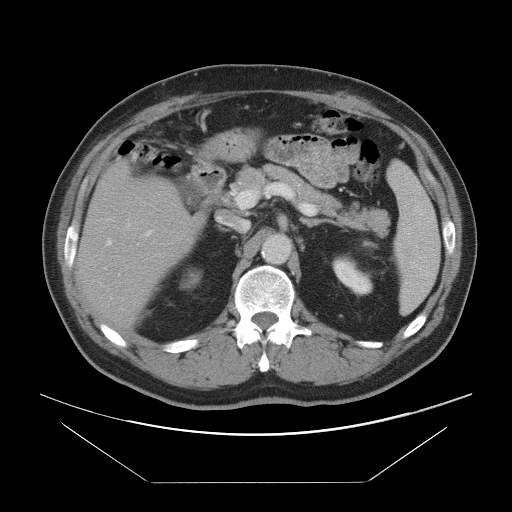
Contrast-enhanced abdominal CT, one axial slice. Position 50 of 97 along the scan axis. 120 kVp. Intravenous contrast given. Soft-tissue window (W 400 / L 40 HU). 5 mm slice thickness. 512 × 512 image matrix, field of view 442 × 442 mm. Male patient, age 62 years. From the clinical record (not read from this slice): diagnosis: colorectal cancer liver metastases, imaged before liver resection; multiple liver metastases: no.
Structures marked on this image (expert manual segmentation):
- hepatic veins: box from (x=106, y=222) to (x=130, y=246) px
- liver: (x=78, y=163)–(x=191, y=328)
- planned liver remnant (the part of the liver to remain after resection): (x=78, y=174)–(x=192, y=328)
- portal vein (with intrahepatic branches): (x=109, y=219)–(x=153, y=236)